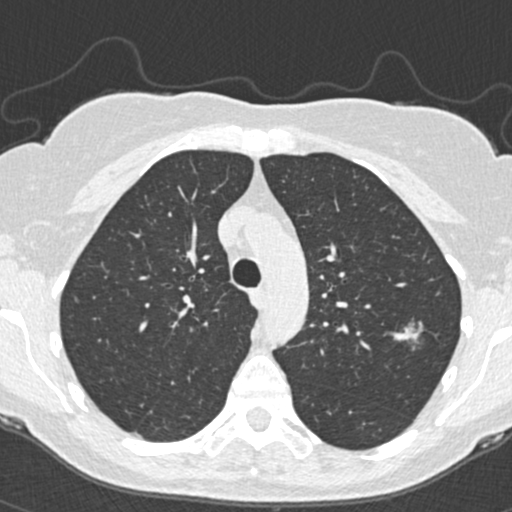
Low-dose screening chest CT, one axial slice; 120 kVp; lung window (W 1500 / L -600 HU); 1 mm slice thickness; 512 × 512 image matrix, field of view 298 × 298 mm.
Outlined on this slice (outlined manually by an expert reader):
- lesion 1 (tumor, upper lobe of left lung): bounding box <393,321,423,343> (left, top, right, bottom; pixels)